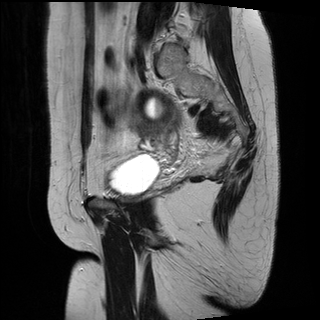
Pelvic MRI for cervical cancer, one sagittal slice; T2-weighted; 1.5 T; TE 89 ms, TR 3320 ms; 320 × 320 image matrix, field of view 260 × 260 mm. Female patient, age 49 years.
Outlined on this slice (manually delineated by an expert):
- uterus and cervix: box from (x=131, y=89) to (x=181, y=141) px